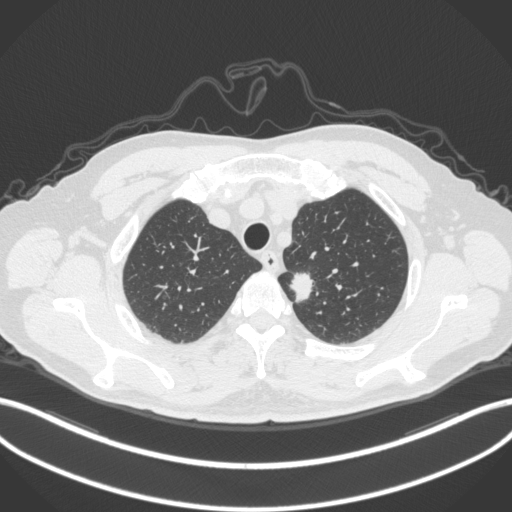
Chest CT, one axial slice. Position 314 of 382 along the scan axis. Lung window (W 1500 / L -600 HU). 512 × 512 image matrix, field of view 400 × 400 mm. Male patient, age 64 years. Case-level facts recorded for this patient, not image findings: clinical TNM (as recorded): T1c N0 M0.
Annotated regions visible in this slice (bounding box drawn by a radiologist):
- lung tumour (recorded histology: adenocarcinoma): box from (x=286, y=268) to (x=323, y=310) px